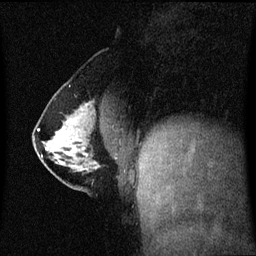
Breast MRI (dynamic contrast-enhanced), one sagittal slice; slice 25 of 60 in the series (ordered by position); dynamic contrast-enhanced series, image 2 of 3 at this slice position (ordered by acquisition); 1.5 T; TE 4.2 ms, TR 8.4 ms; 256 × 256 image matrix, field of view 210 × 210 mm. Patient: female, 40 years. Case-level facts recorded for this patient, not image findings: setting: breast cancer imaged before/during neoadjuvant chemotherapy; receptor status: triple-negative.
Structures marked on this image (semi-automatic segmentation, software-assisted and operator-edited):
- analysis volume of interest (the breast-tissue region the enhancement analysis was run in; not a lesion): bounding box [x1, y1, x2, y2] px = [33, 112, 124, 188]
- tumour enhancement mask (voxels above the 70 % enhancement threshold inside the analysis volume of interest): [38, 130, 65, 151]